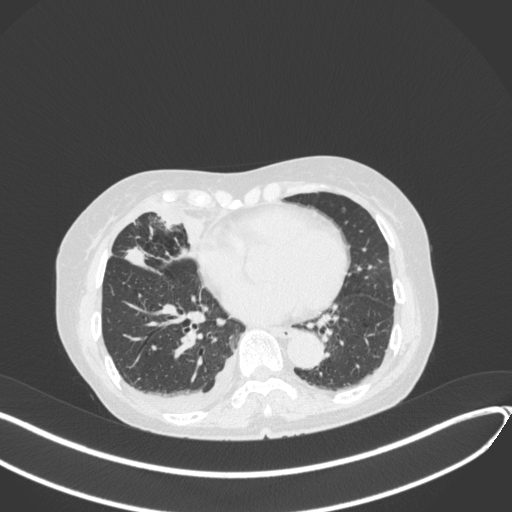
Chest CT, one axial slice. Slice 155 of 418 in the series (ordered by position). Reconstruction kernel B31f. Lung window (W 1500 / L -600 HU). 512 × 512 image matrix. Female patient, age 75 years. From the clinical record (not read from this slice): clinical TNM (as recorded): T2a N3 M0.
Outlined on this slice (rectangle marked by the reading radiologist):
- lung tumour (recorded histology: adenocarcinoma): bounding box (x1, y1, x2, y2) in pixels: (122, 242, 148, 268)